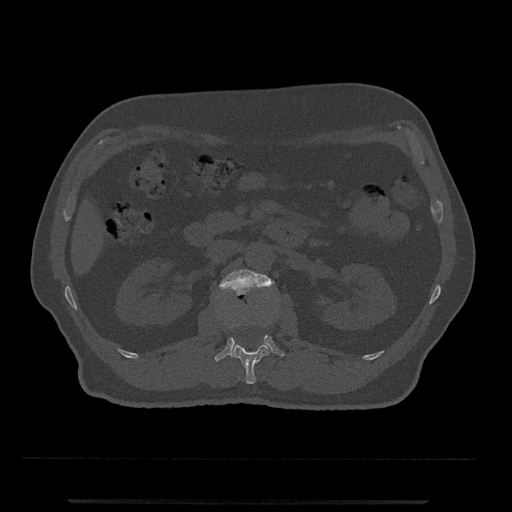
CT including the spine, one axial slice; position 303 of 797 along the scan axis; reconstruction kernel Br40s/3; 120 kVp; bone window (W 1800 / L 400 HU); 0.5 mm slice thickness; 512 × 512 image matrix, field of view 419 × 419 mm. Male patient, age 63 years. Case-level facts recorded for this patient, not image findings: primary cancer: prostate.
Outlined on this slice (semi-automatic segmentation, software-assisted and operator-edited):
- L1 vertebra: bounding box <232,322,270,384> (left, top, right, bottom; pixels)
- L2 vertebra: <214,269,285,362>